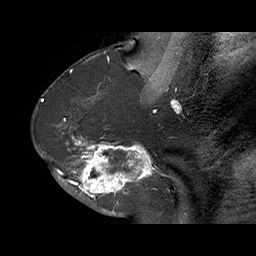
Breast MRI (dynamic contrast-enhanced), one sagittal slice; slice 34 of 70 in the series (ordered by position); dynamic contrast-enhanced series, time point 2 of 6 at this slice position (early post-contrast); 1.5 T; TE 4.5 ms, TR 32.4 ms; 256 × 256 image matrix. Female patient. From the clinical record (not read from this slice): setting: breast cancer imaged before/during neoadjuvant chemotherapy; receptor status: HR-positive, HER2-negative.
Structures marked on this image (semi-automatically segmented with operator editing):
- analysis volume of interest (the breast-tissue region the enhancement analysis was run in; not a lesion): bounding box (x1, y1, x2, y2) in pixels: (71, 128, 159, 202)
- tumour enhancement mask (voxels above the 100 % enhancement threshold inside the analysis volume of interest): (71, 135, 156, 201)